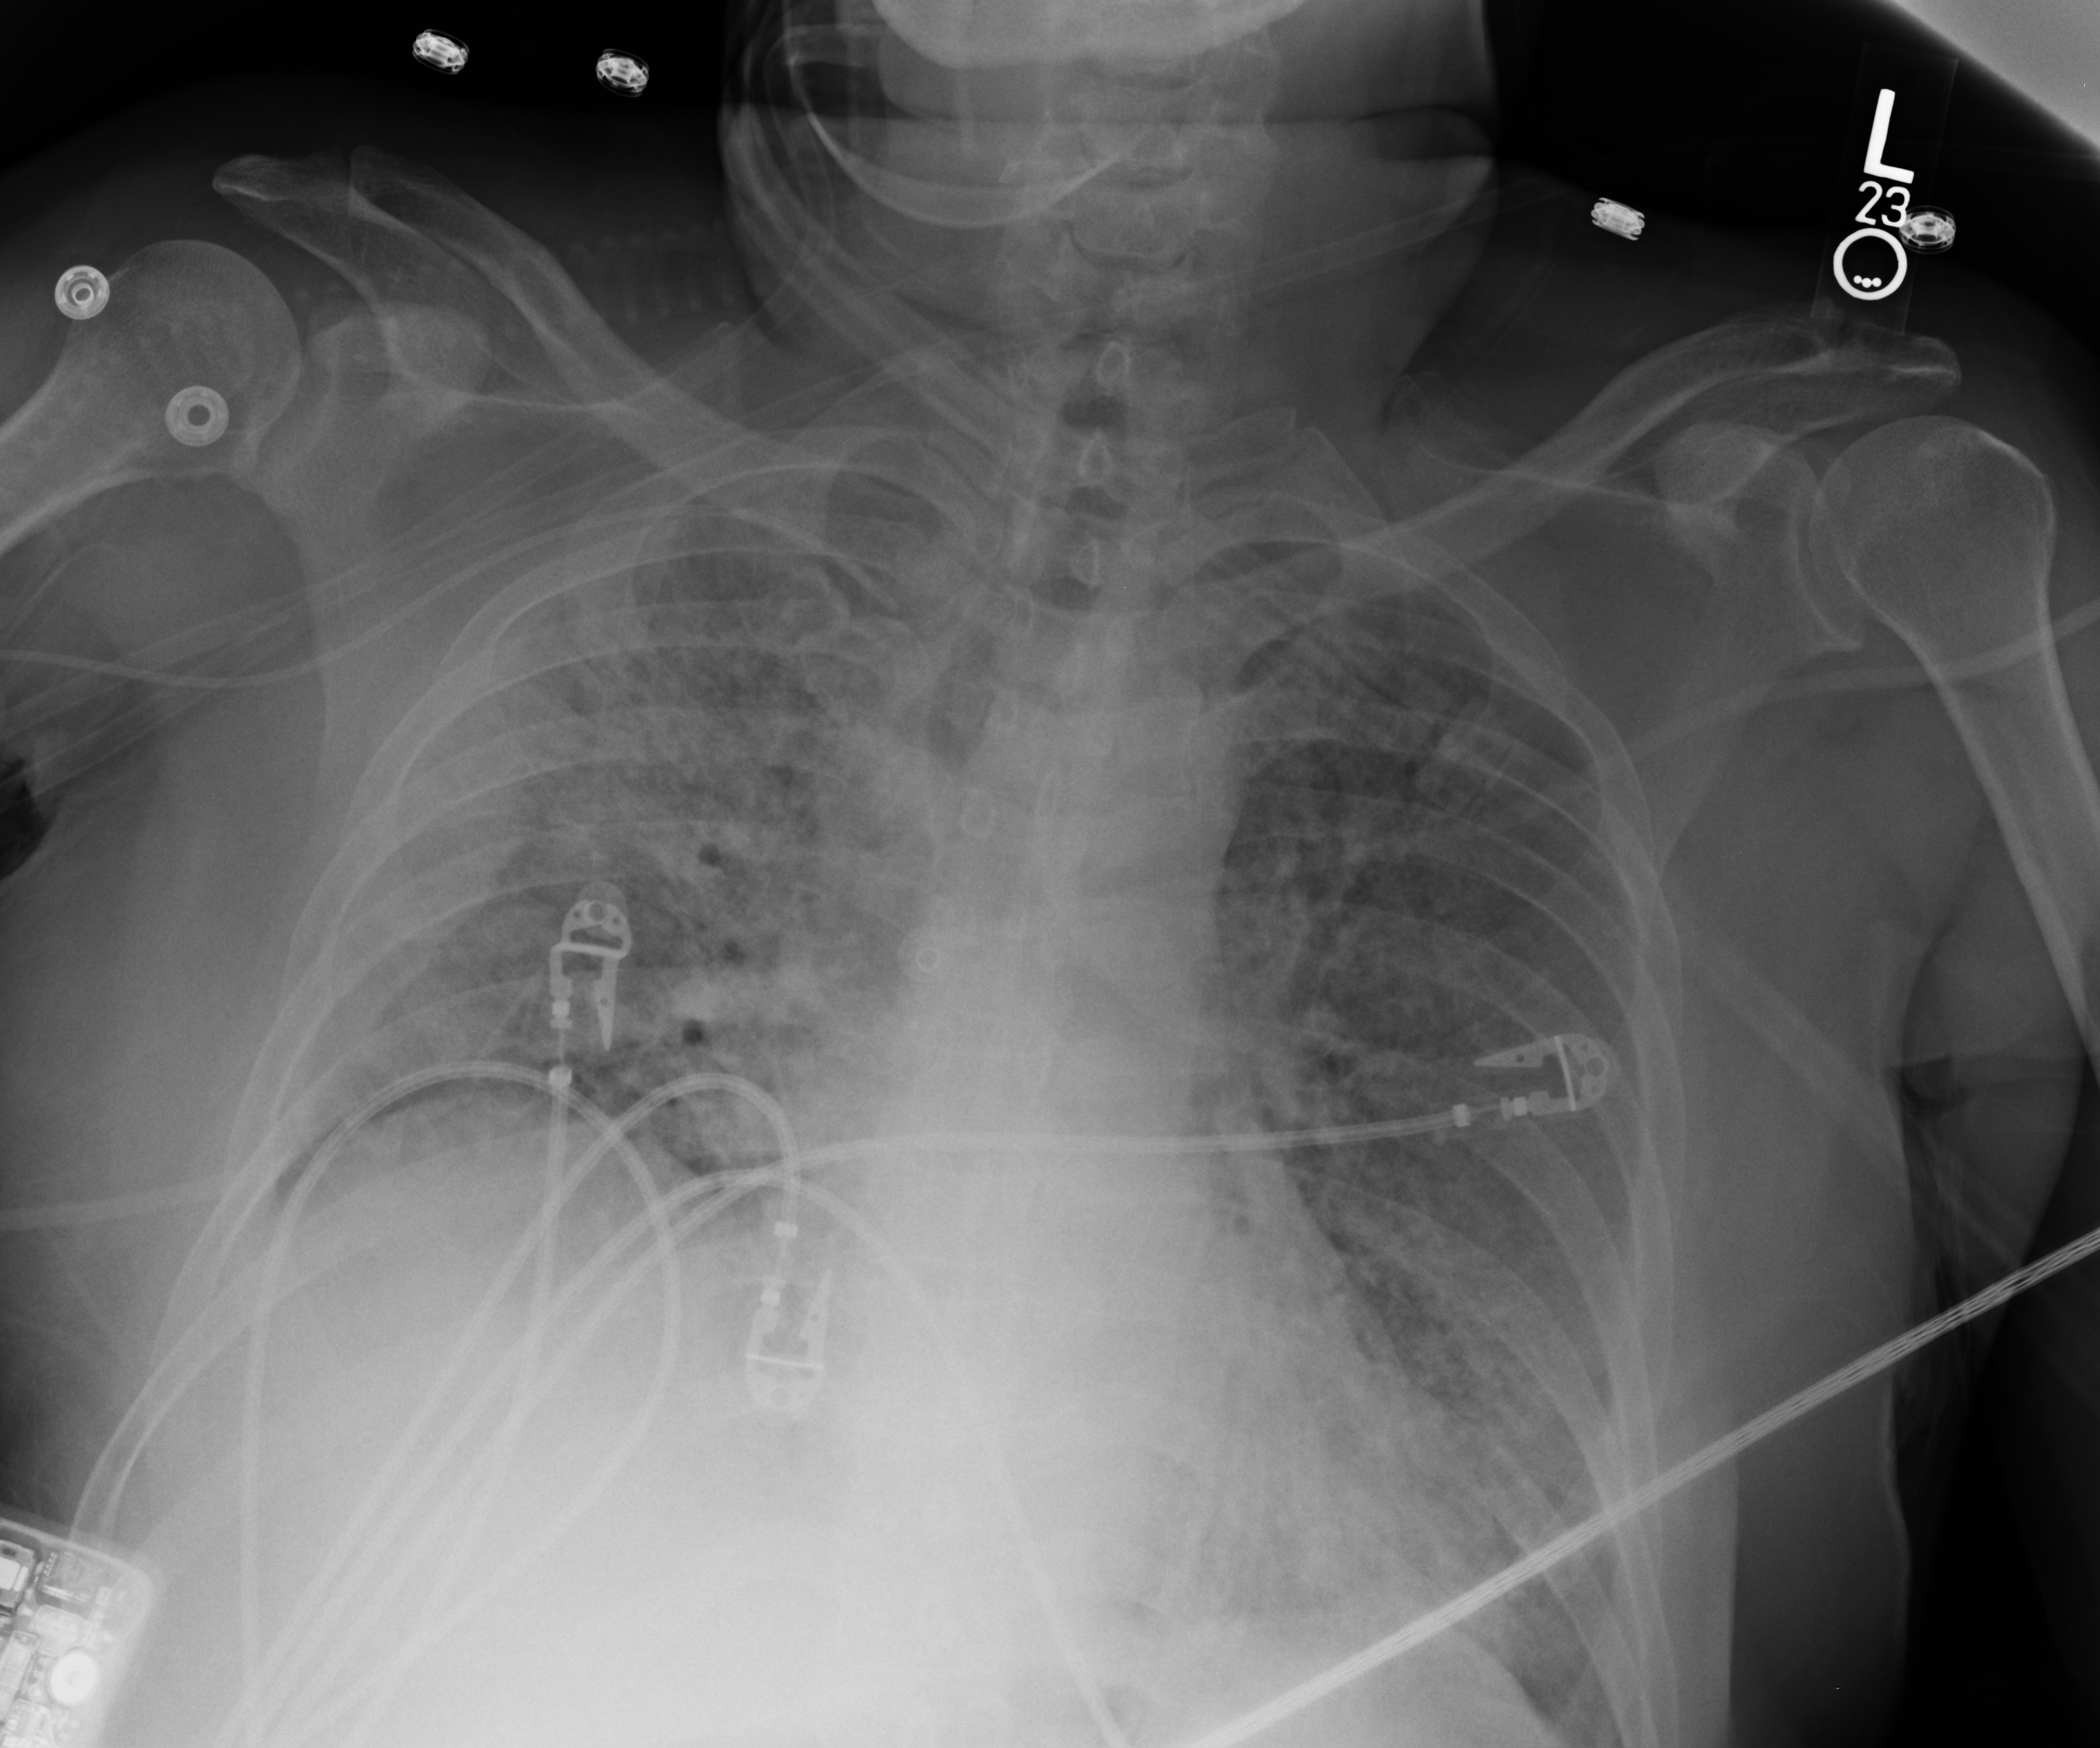
Portable chest radiograph; anteroposterior (AP) projection. Male patient hospitalised with COVID-19, age 18–59 years.
Admission-level facts for this patient (not findings on this image; timing relative to this image not recorded): admitted to intensive care during this hospital stay: yes; mechanically ventilated during this hospital stay: yes.